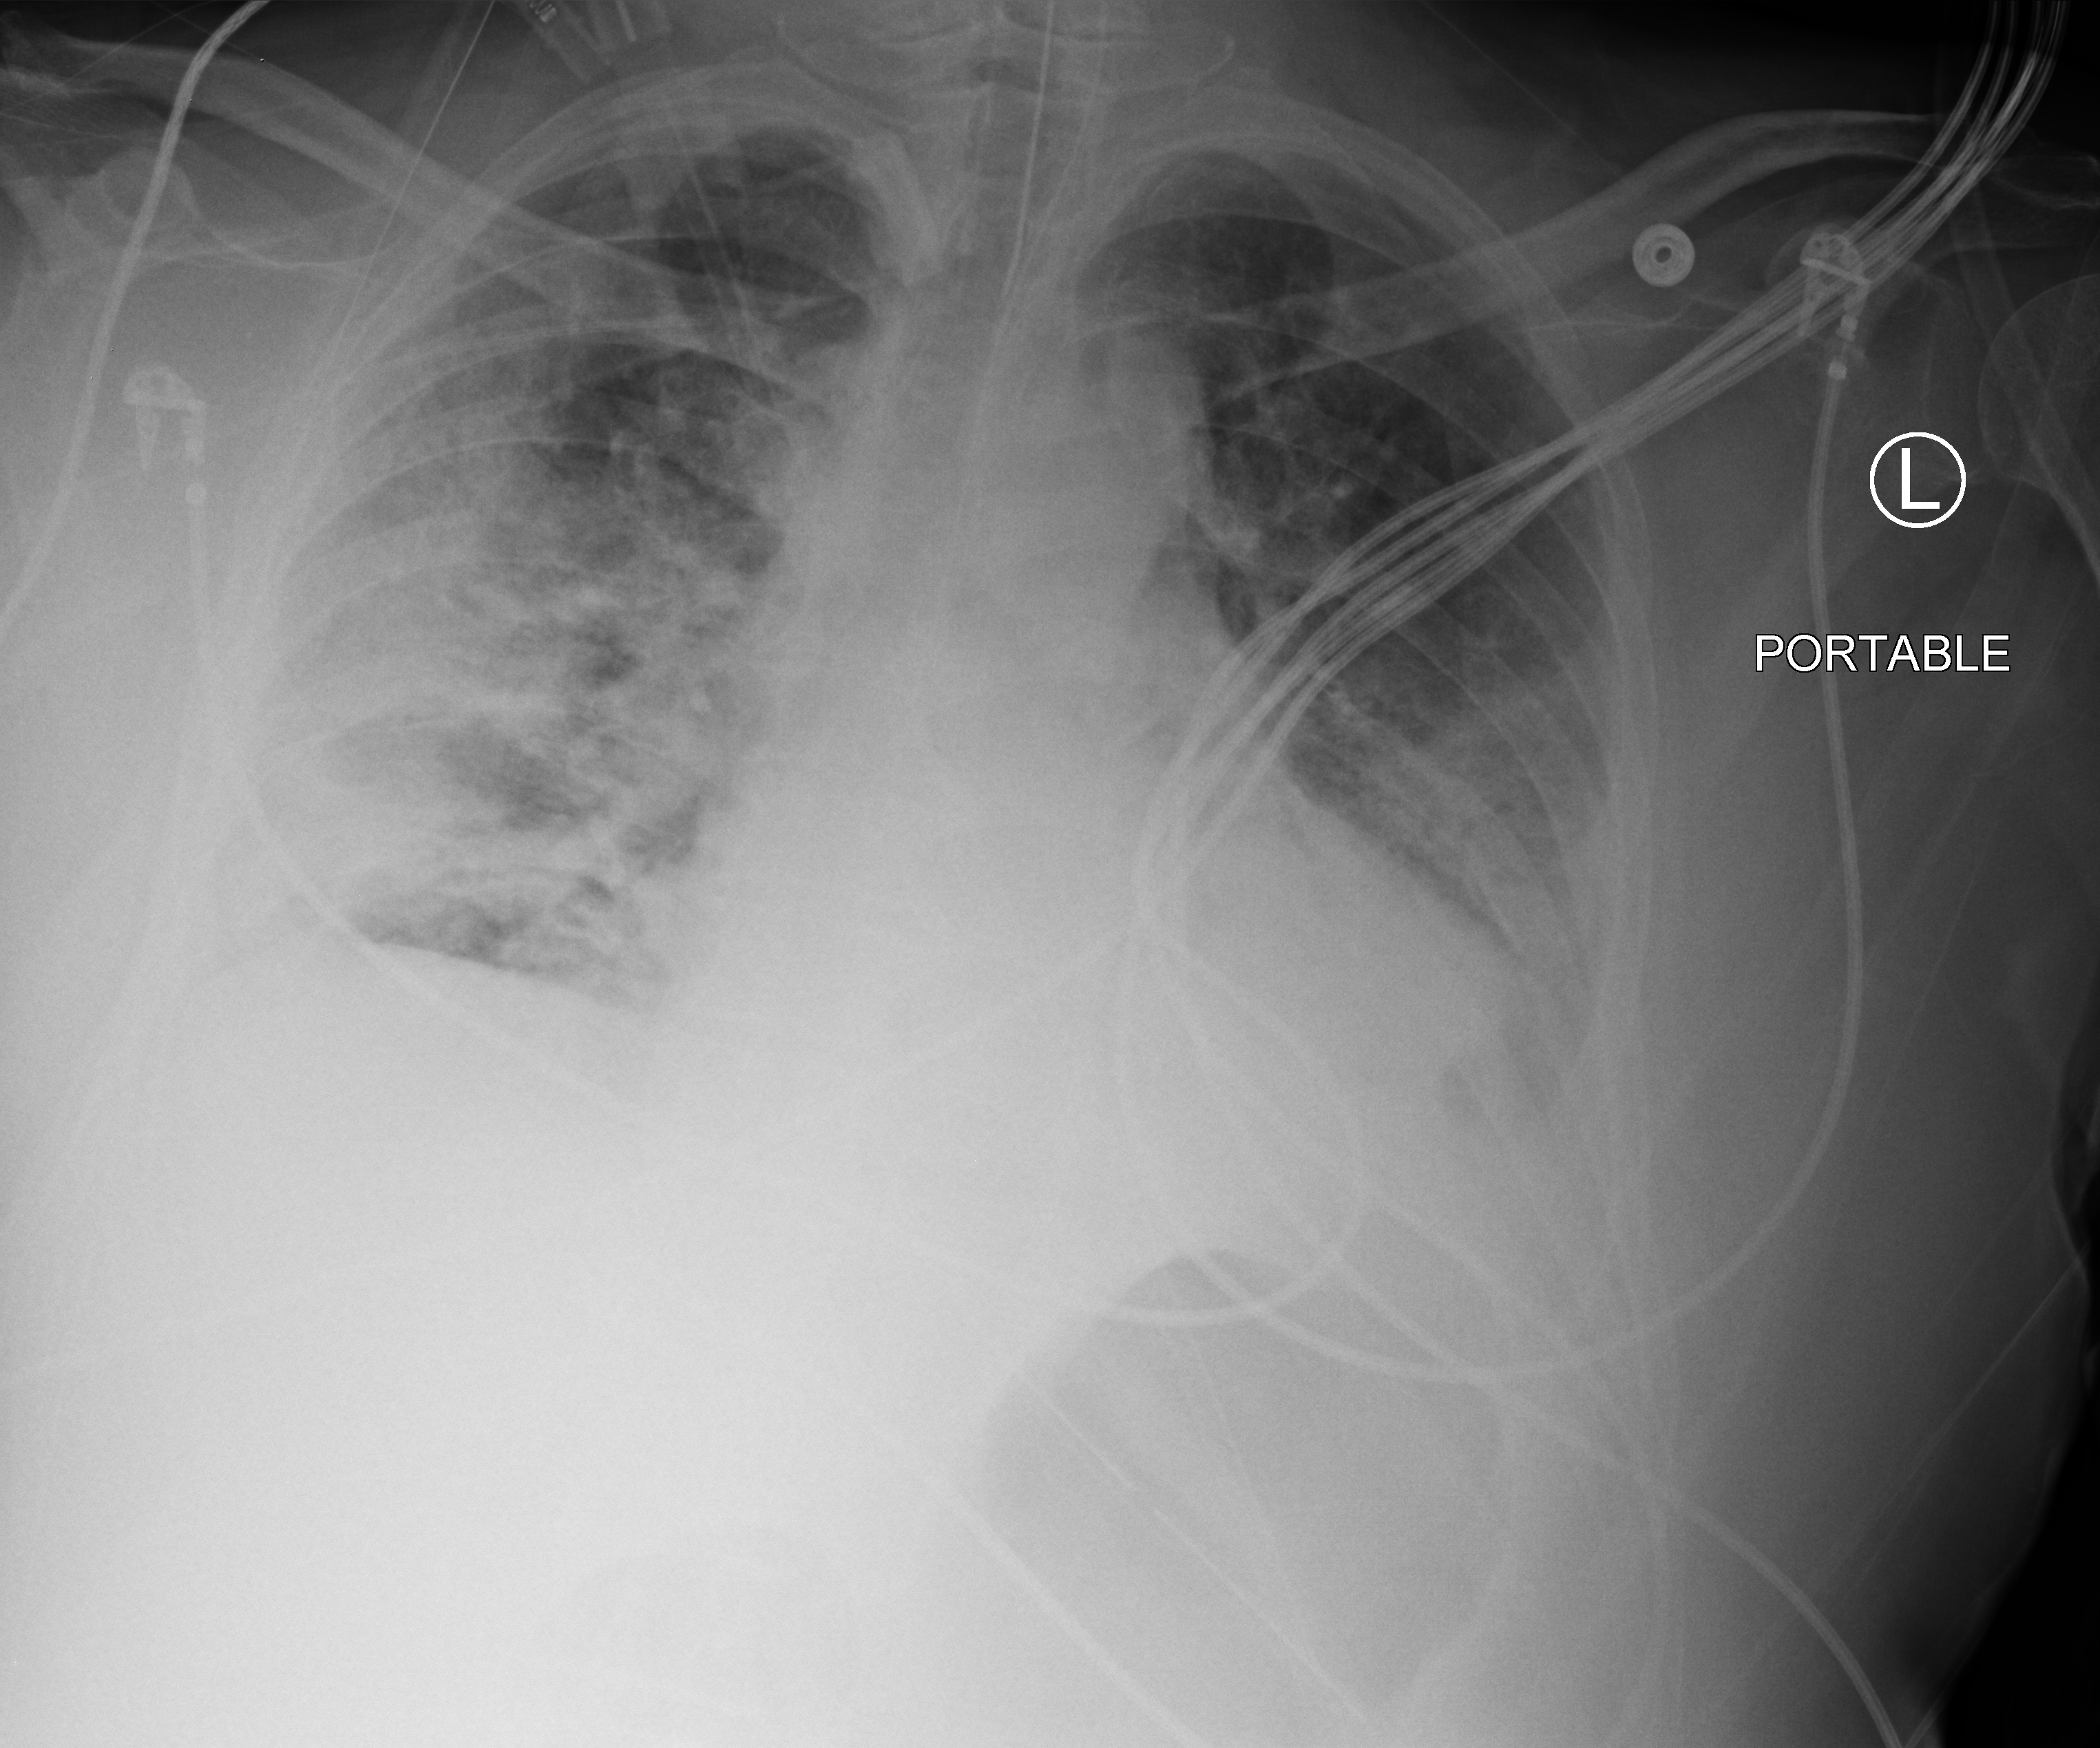
Portable chest radiograph; anteroposterior (AP) projection. Male patient hospitalised with COVID-19, age 60–74 years.
Admission-level facts for this patient (not findings on this image; timing relative to this image not recorded):
- mechanically ventilated during this hospital stay: yes
- admitted to intensive care during this hospital stay: yes
- hypertension (admission record): yes